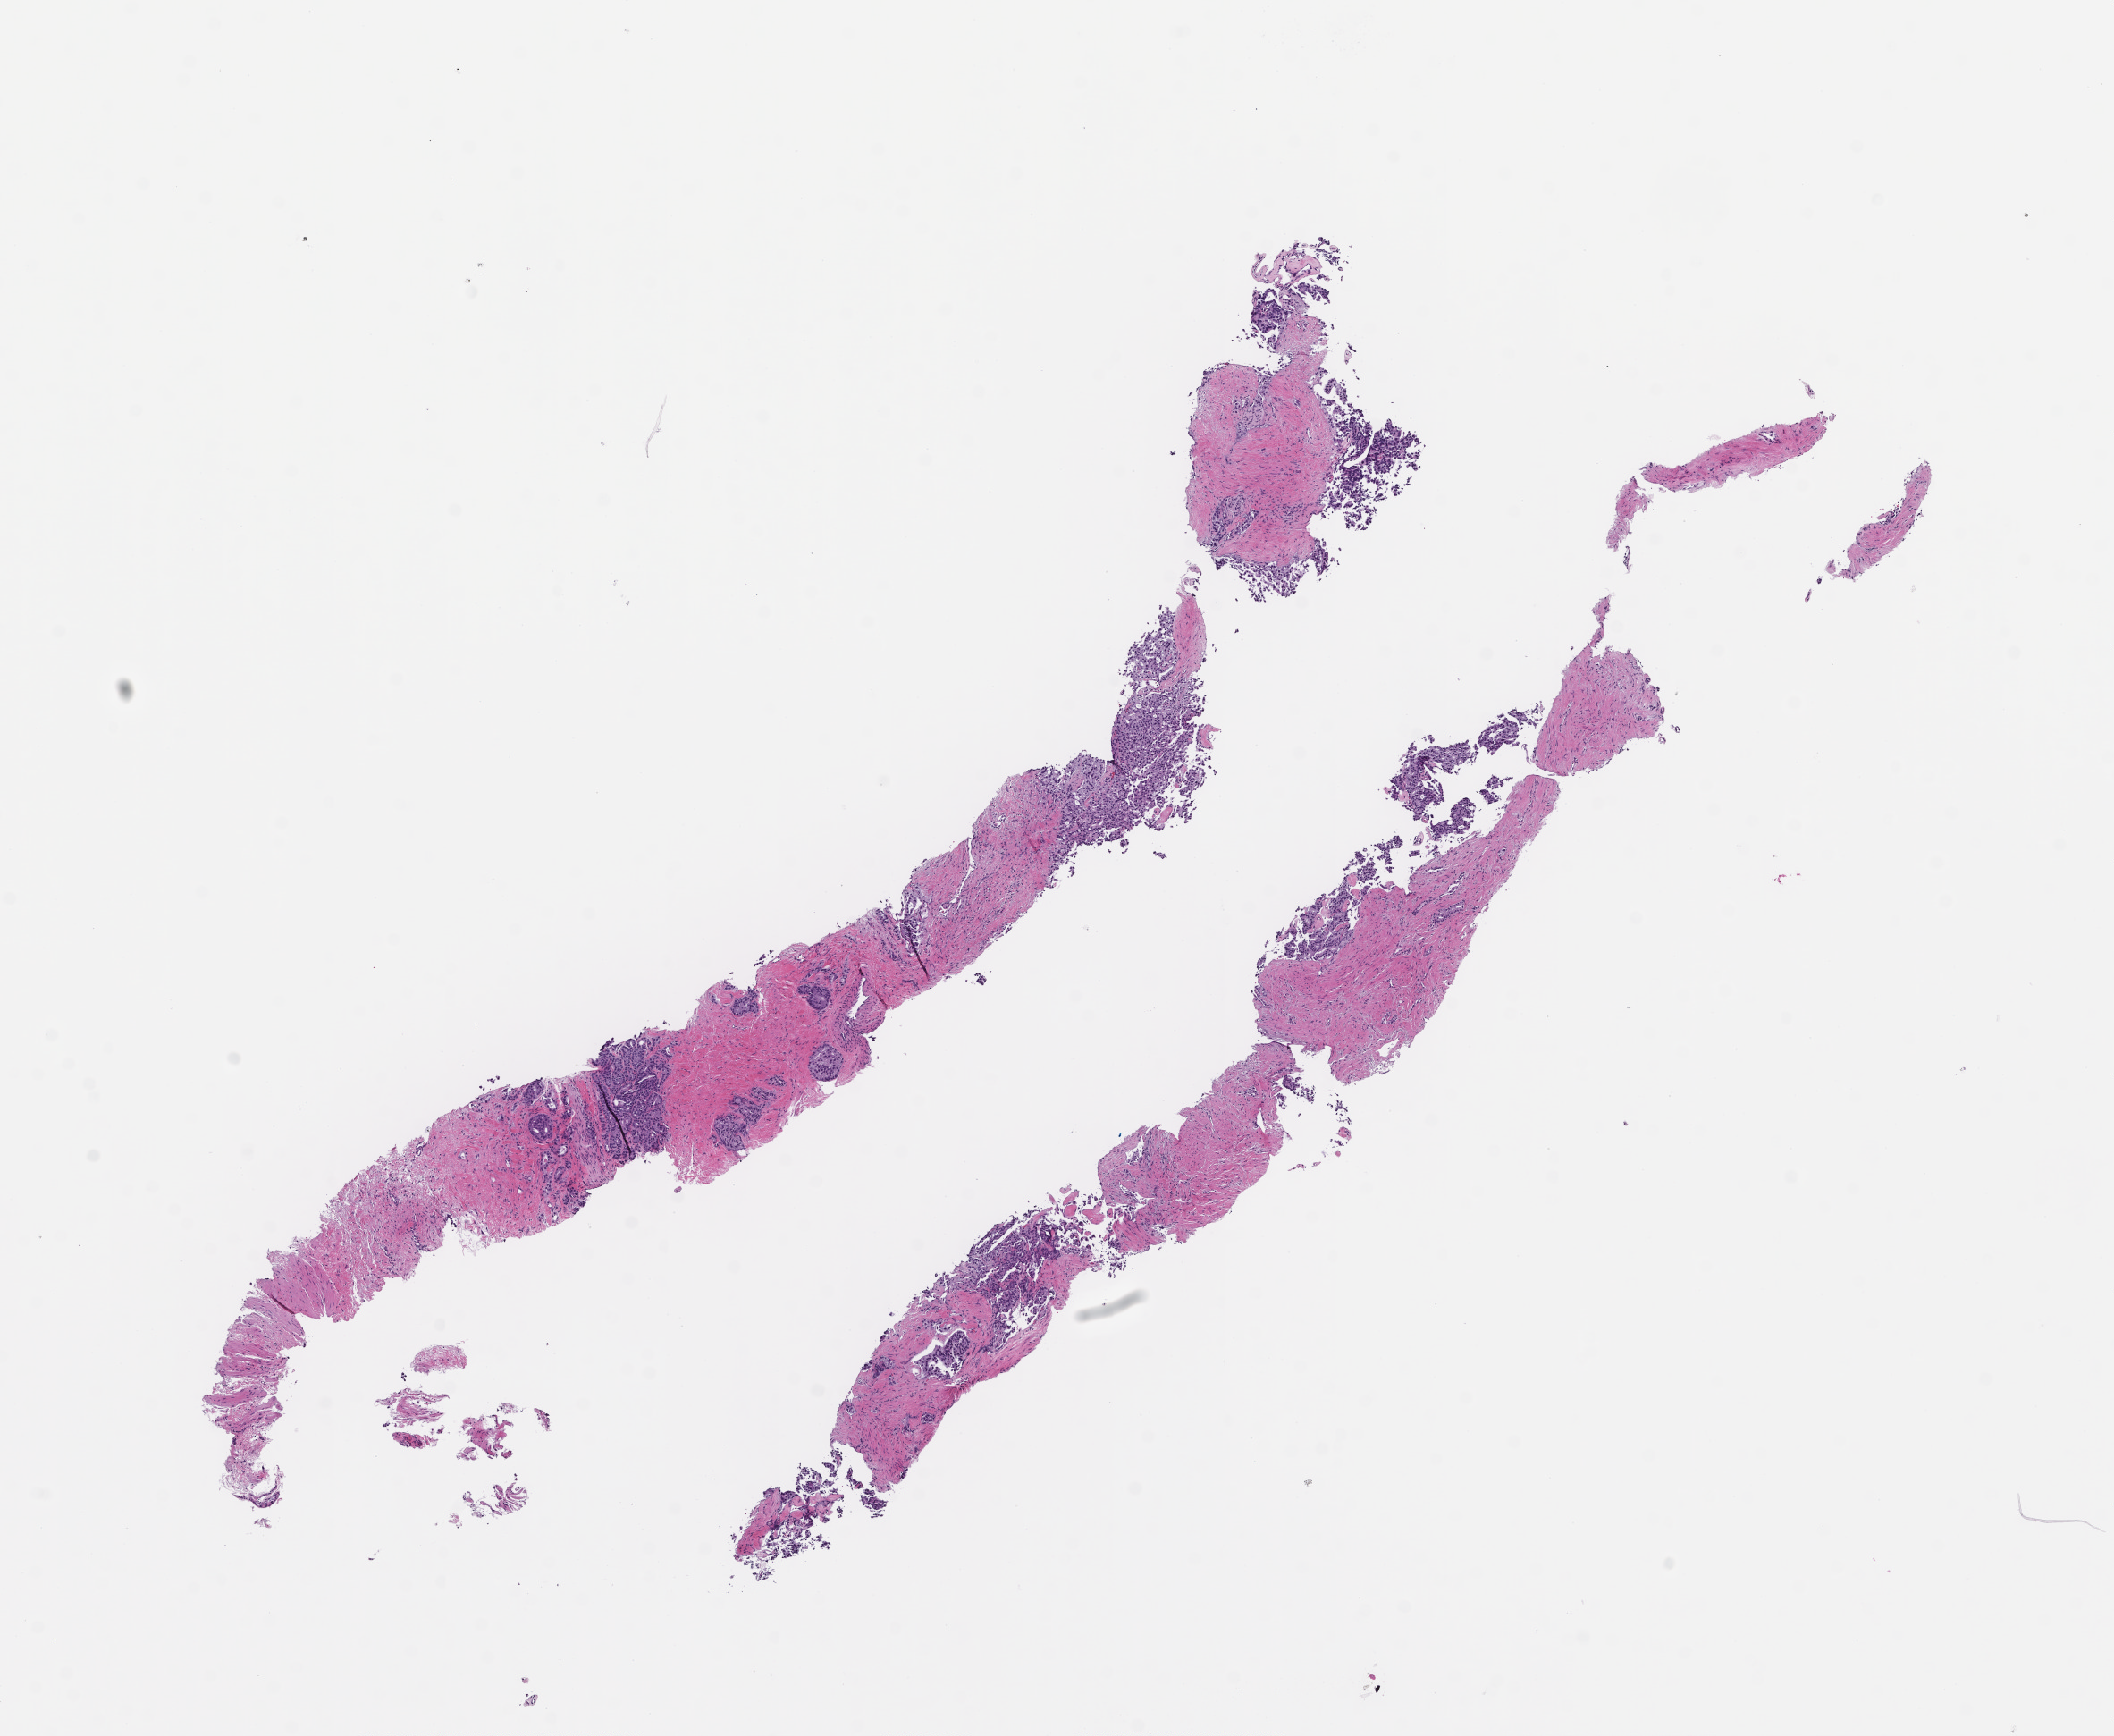
Whole-slide image, haematoxylin and eosin stain — whole scanned area (about 9.5 x 7.8 mm) shown as a low-resolution overview, FFPE section, tissue site: prostate, specimen time point: archival tissue. Patient: male.
• this section: primary tumor
• diagnosis: Prostate Carcinoma